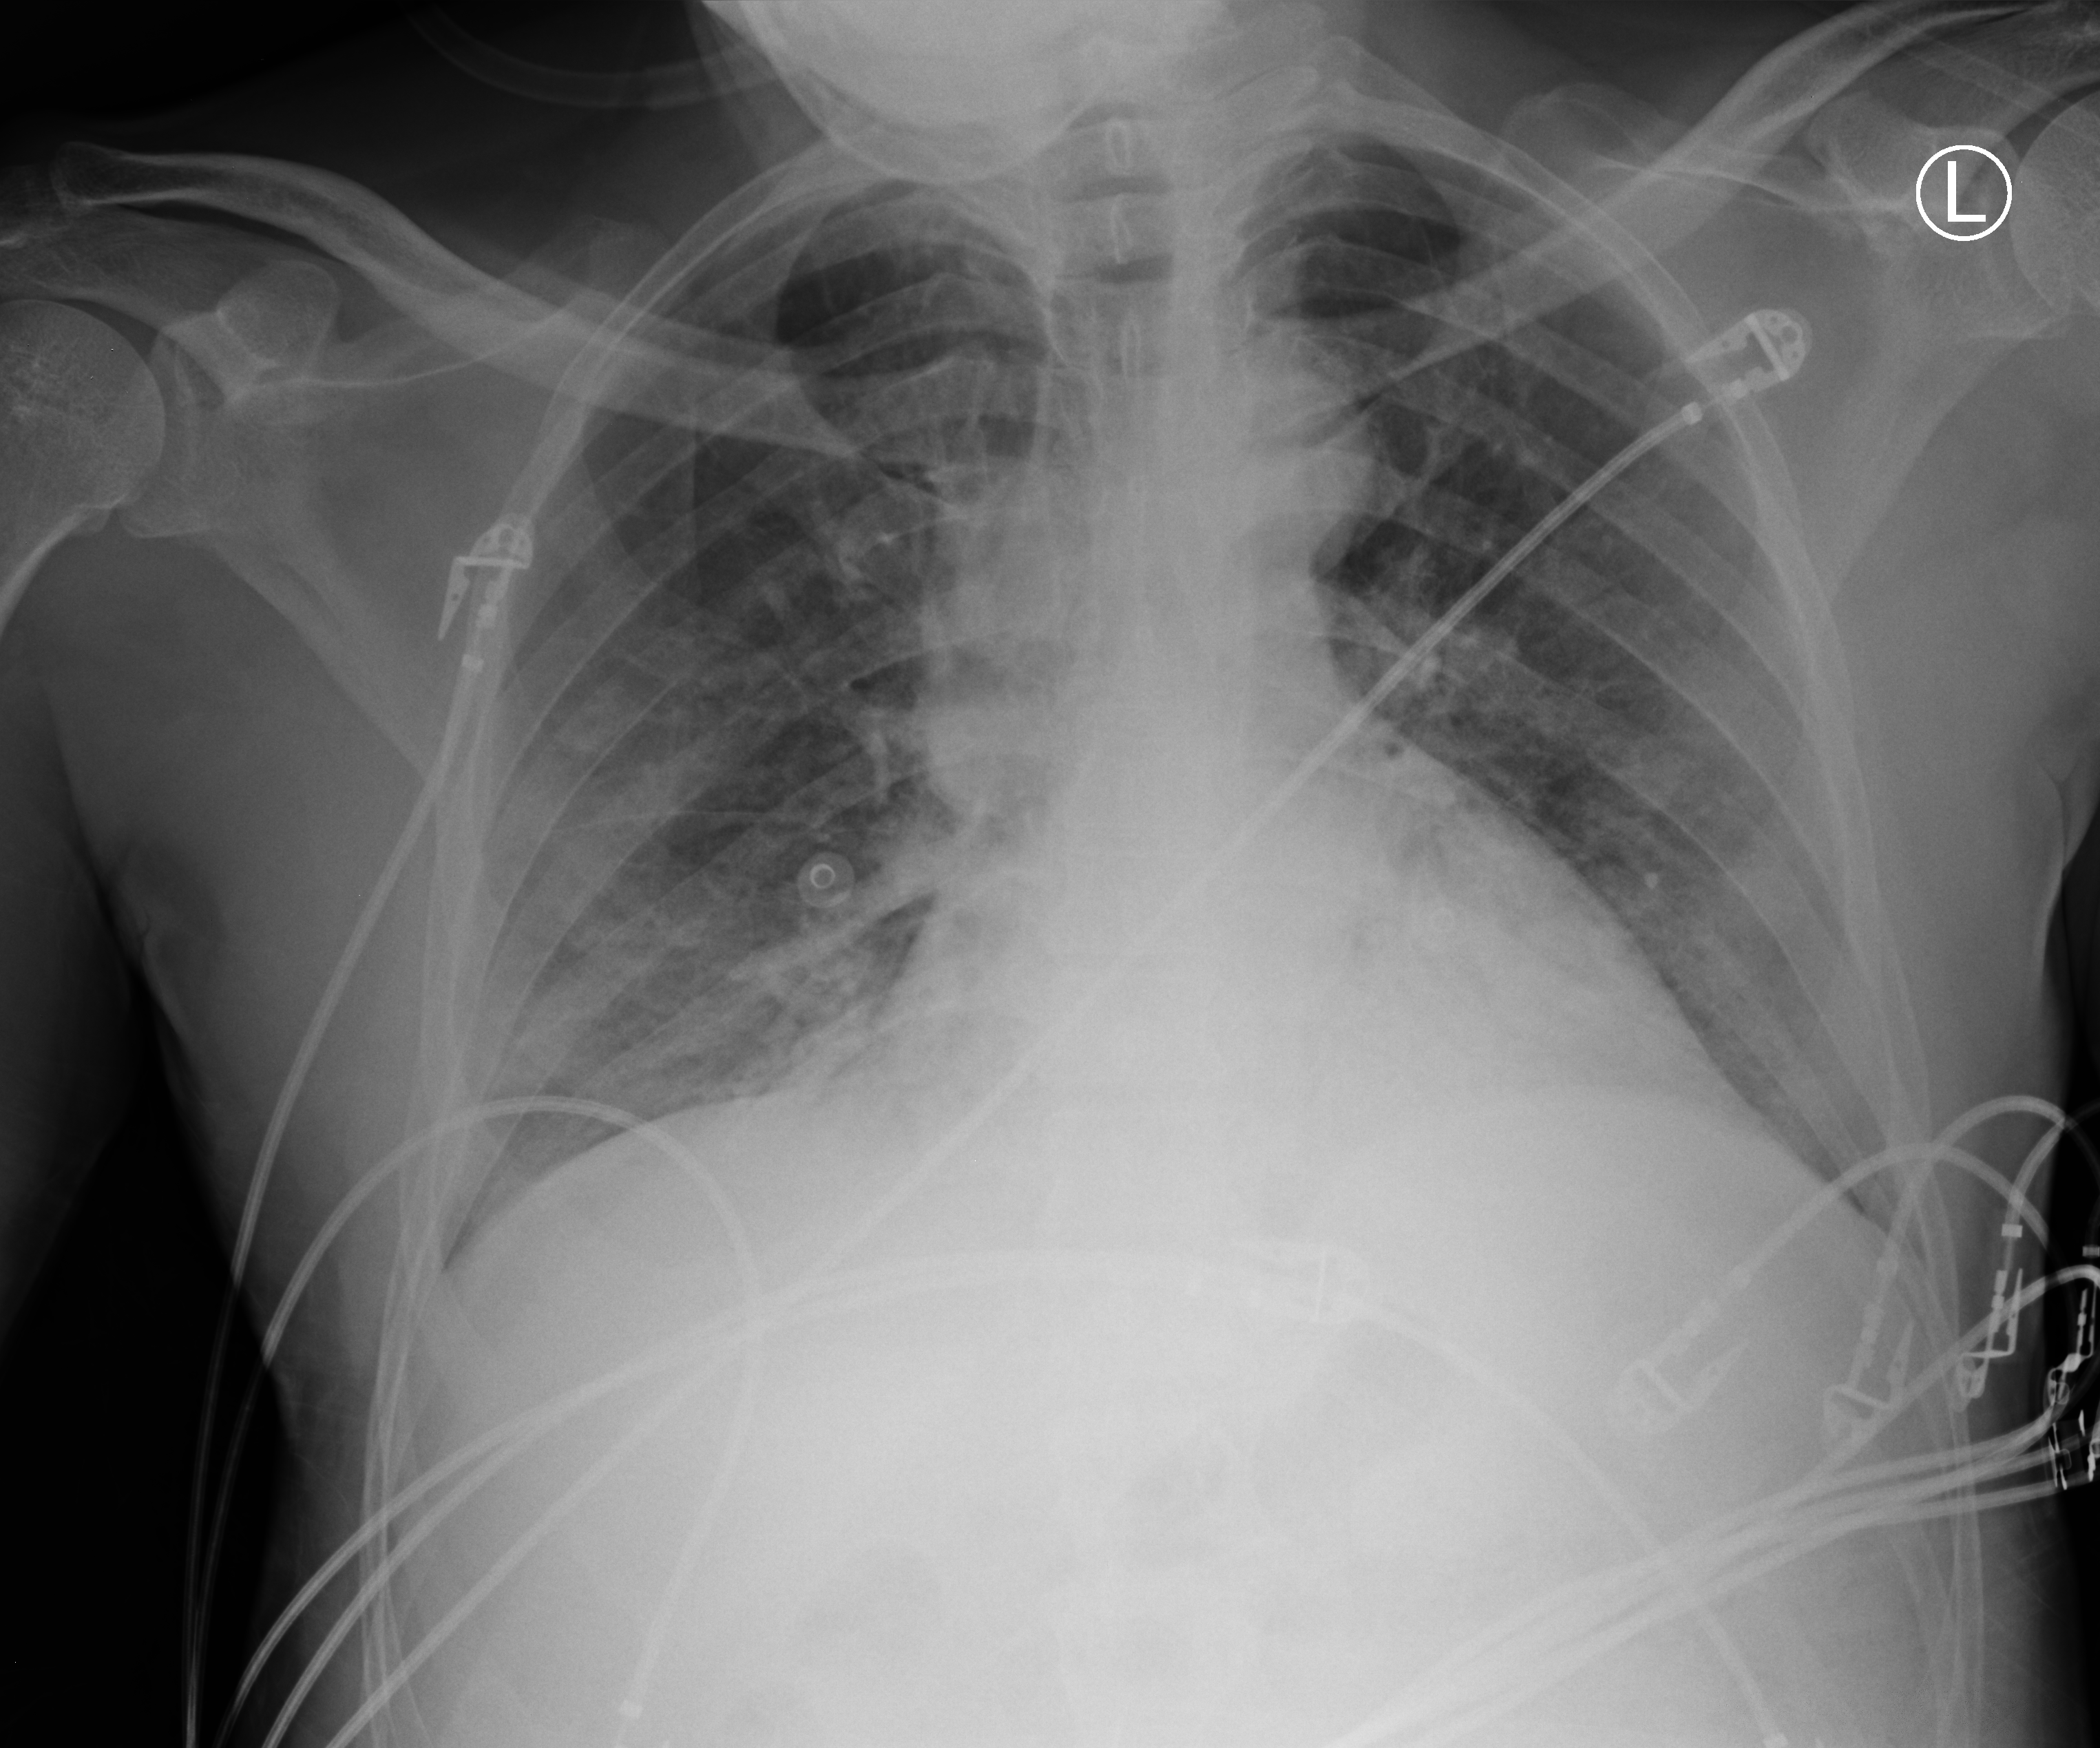
Portable chest radiograph; anteroposterior (AP) projection. Male patient hospitalised with COVID-19, age 18–59 years.
From the hospital-stay record, not from the radiograph (when in the stay this image was taken is not recorded): mechanically ventilated during this hospital stay: yes; other chronic lung disease (admission record): no.